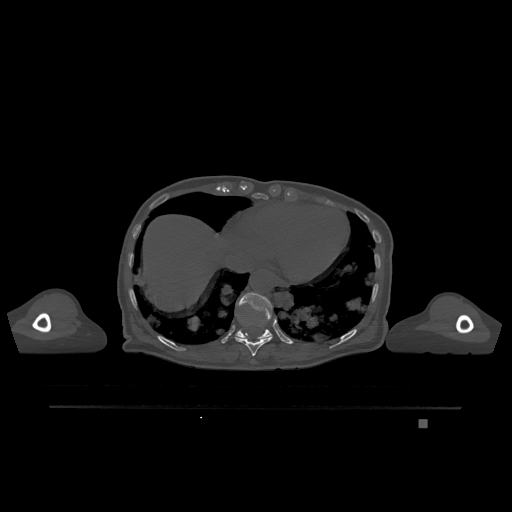
CT including the spine, one axial slice. Position 622 of 1317 along the scan axis. Bone window (W 1800 / L 400 HU). 0.5 mm slice thickness. 512 × 512 image matrix, field of view 500 × 500 mm. Patient: female, 74 years. Case-level facts recorded for this patient, not image findings: primary cancer: lung.
Outlined on this slice (semi-automatic segmentation, software-assisted and operator-edited):
- T10 vertebra: bounding box (x1, y1, x2, y2) in pixels: (235, 333, 273, 356)
- T11 vertebra: (235, 292, 273, 339)